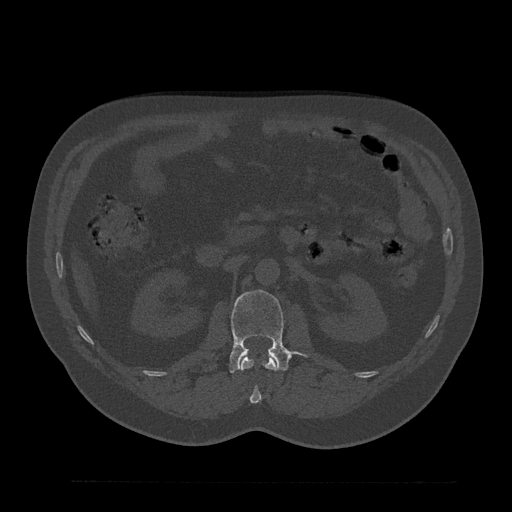
CT including the spine, one axial slice. Slice 120 of 797 in the series (ordered by position). Reconstruction kernel Br40s/3. 120 kVp. Bone window (W 1800 / L 400 HU). 0.5 mm slice thickness. 512 × 512 image matrix, field of view 430 × 430 mm. Male patient, age 61 years. From the clinical record (not read from this slice): primary cancer: prostate.
Structures marked on this image (semi-automatic segmentation, software-assisted and operator-edited):
- L1 vertebra: box from (x=240, y=354) to (x=278, y=404) px
- L2 vertebra: (x=229, y=290)–(x=291, y=373)